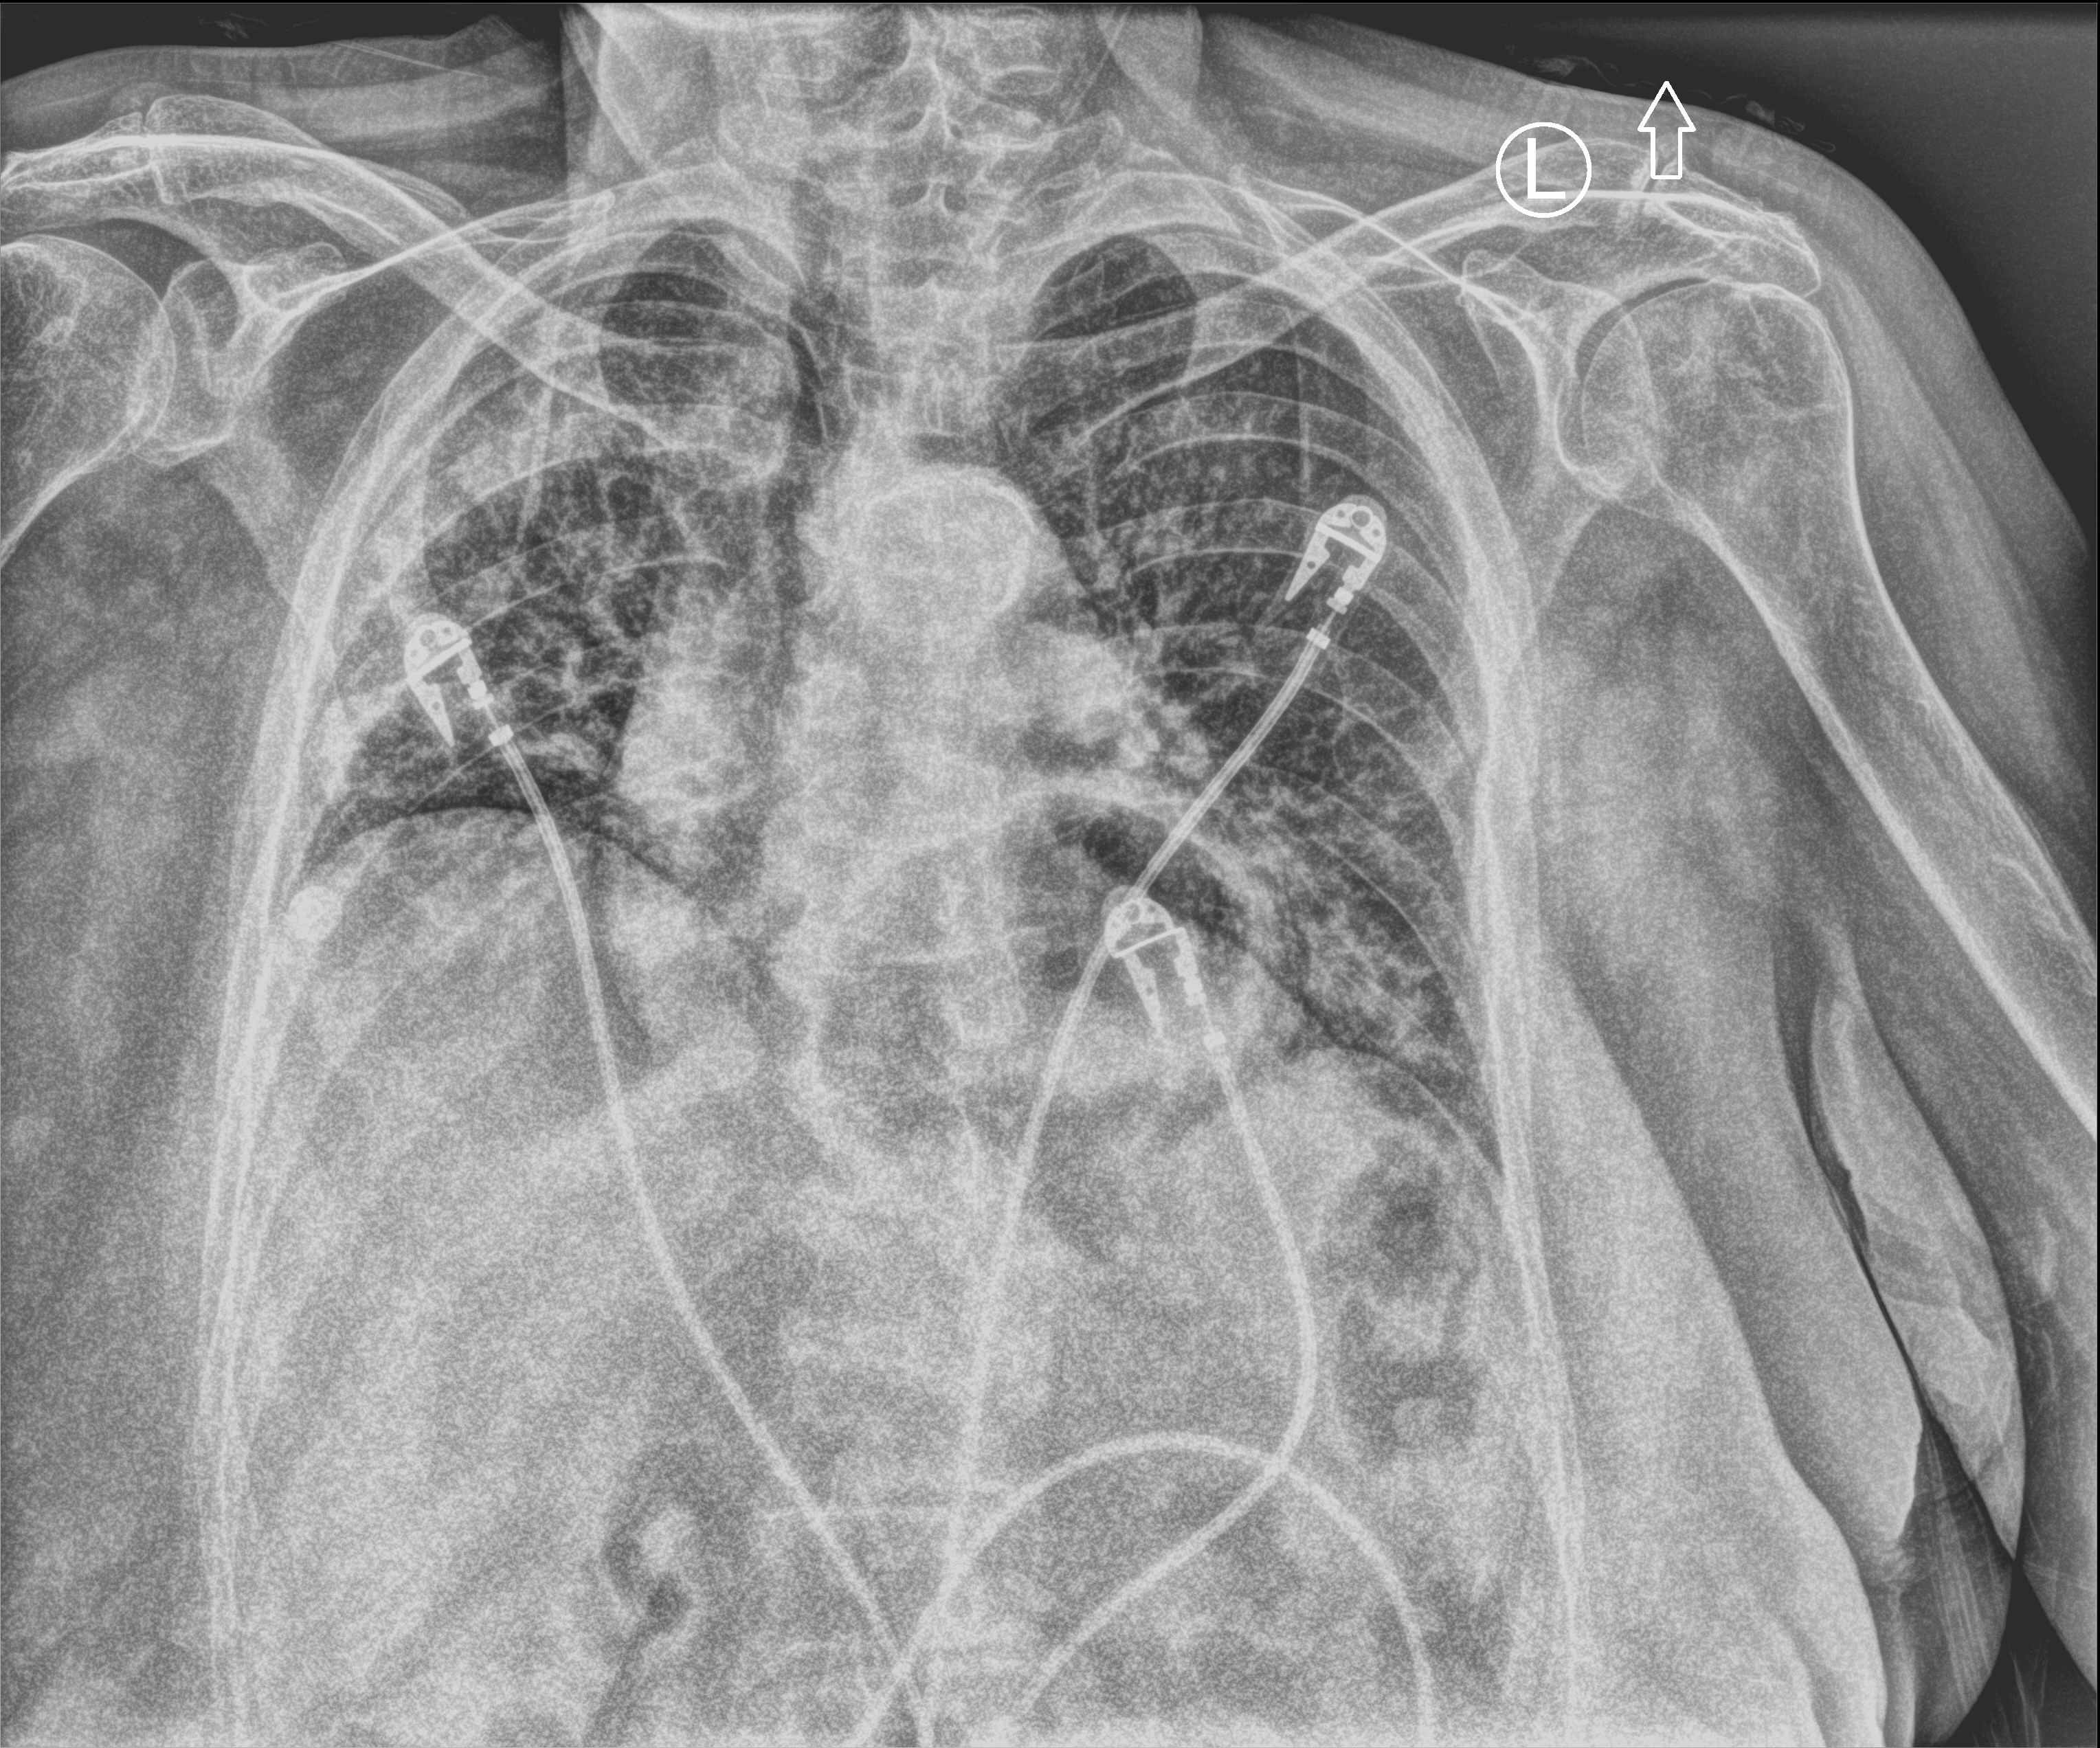
Chest X-ray (portable), anteroposterior (AP) projection. Patient hospitalised with COVID-19; female, aged 75–90 years.
Hospital-stay facts (about this admission, not read from this image; timing relative to this image not recorded):
- other chronic lung disease (admission record): no
- length of hospital stay: 12 days
- mechanically ventilated during this hospital stay: no